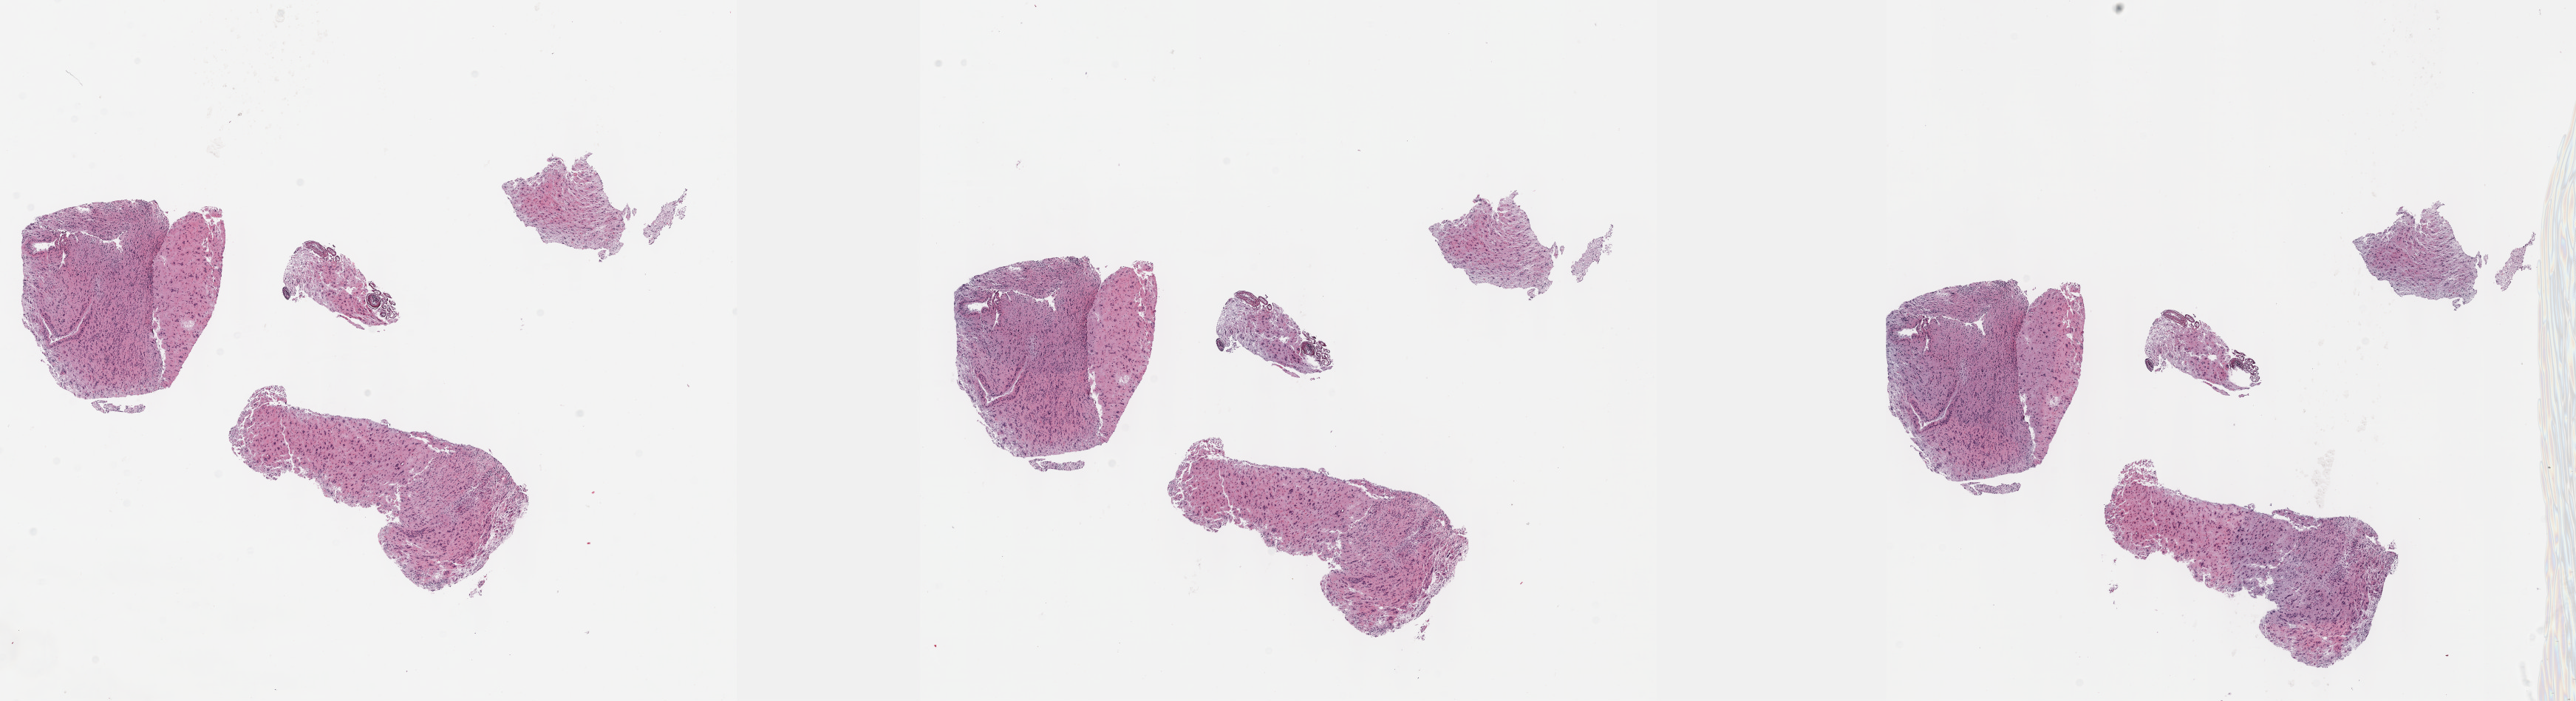
H&E whole-slide image — shown as a low-resolution overview of the whole scanned area (about 28.2 x 7.7 mm, from a 40x scan). Formalin-fixed paraffin-embedded (FFPE) diagnostic section. Sample: primary tumour, brain. Female, age 45 years at initial diagnosis. Histologic grade: G3 (poorly differentiated).
Diagnosis: Astrocytoma, anaplastic (cerebrum). Laterality: right.